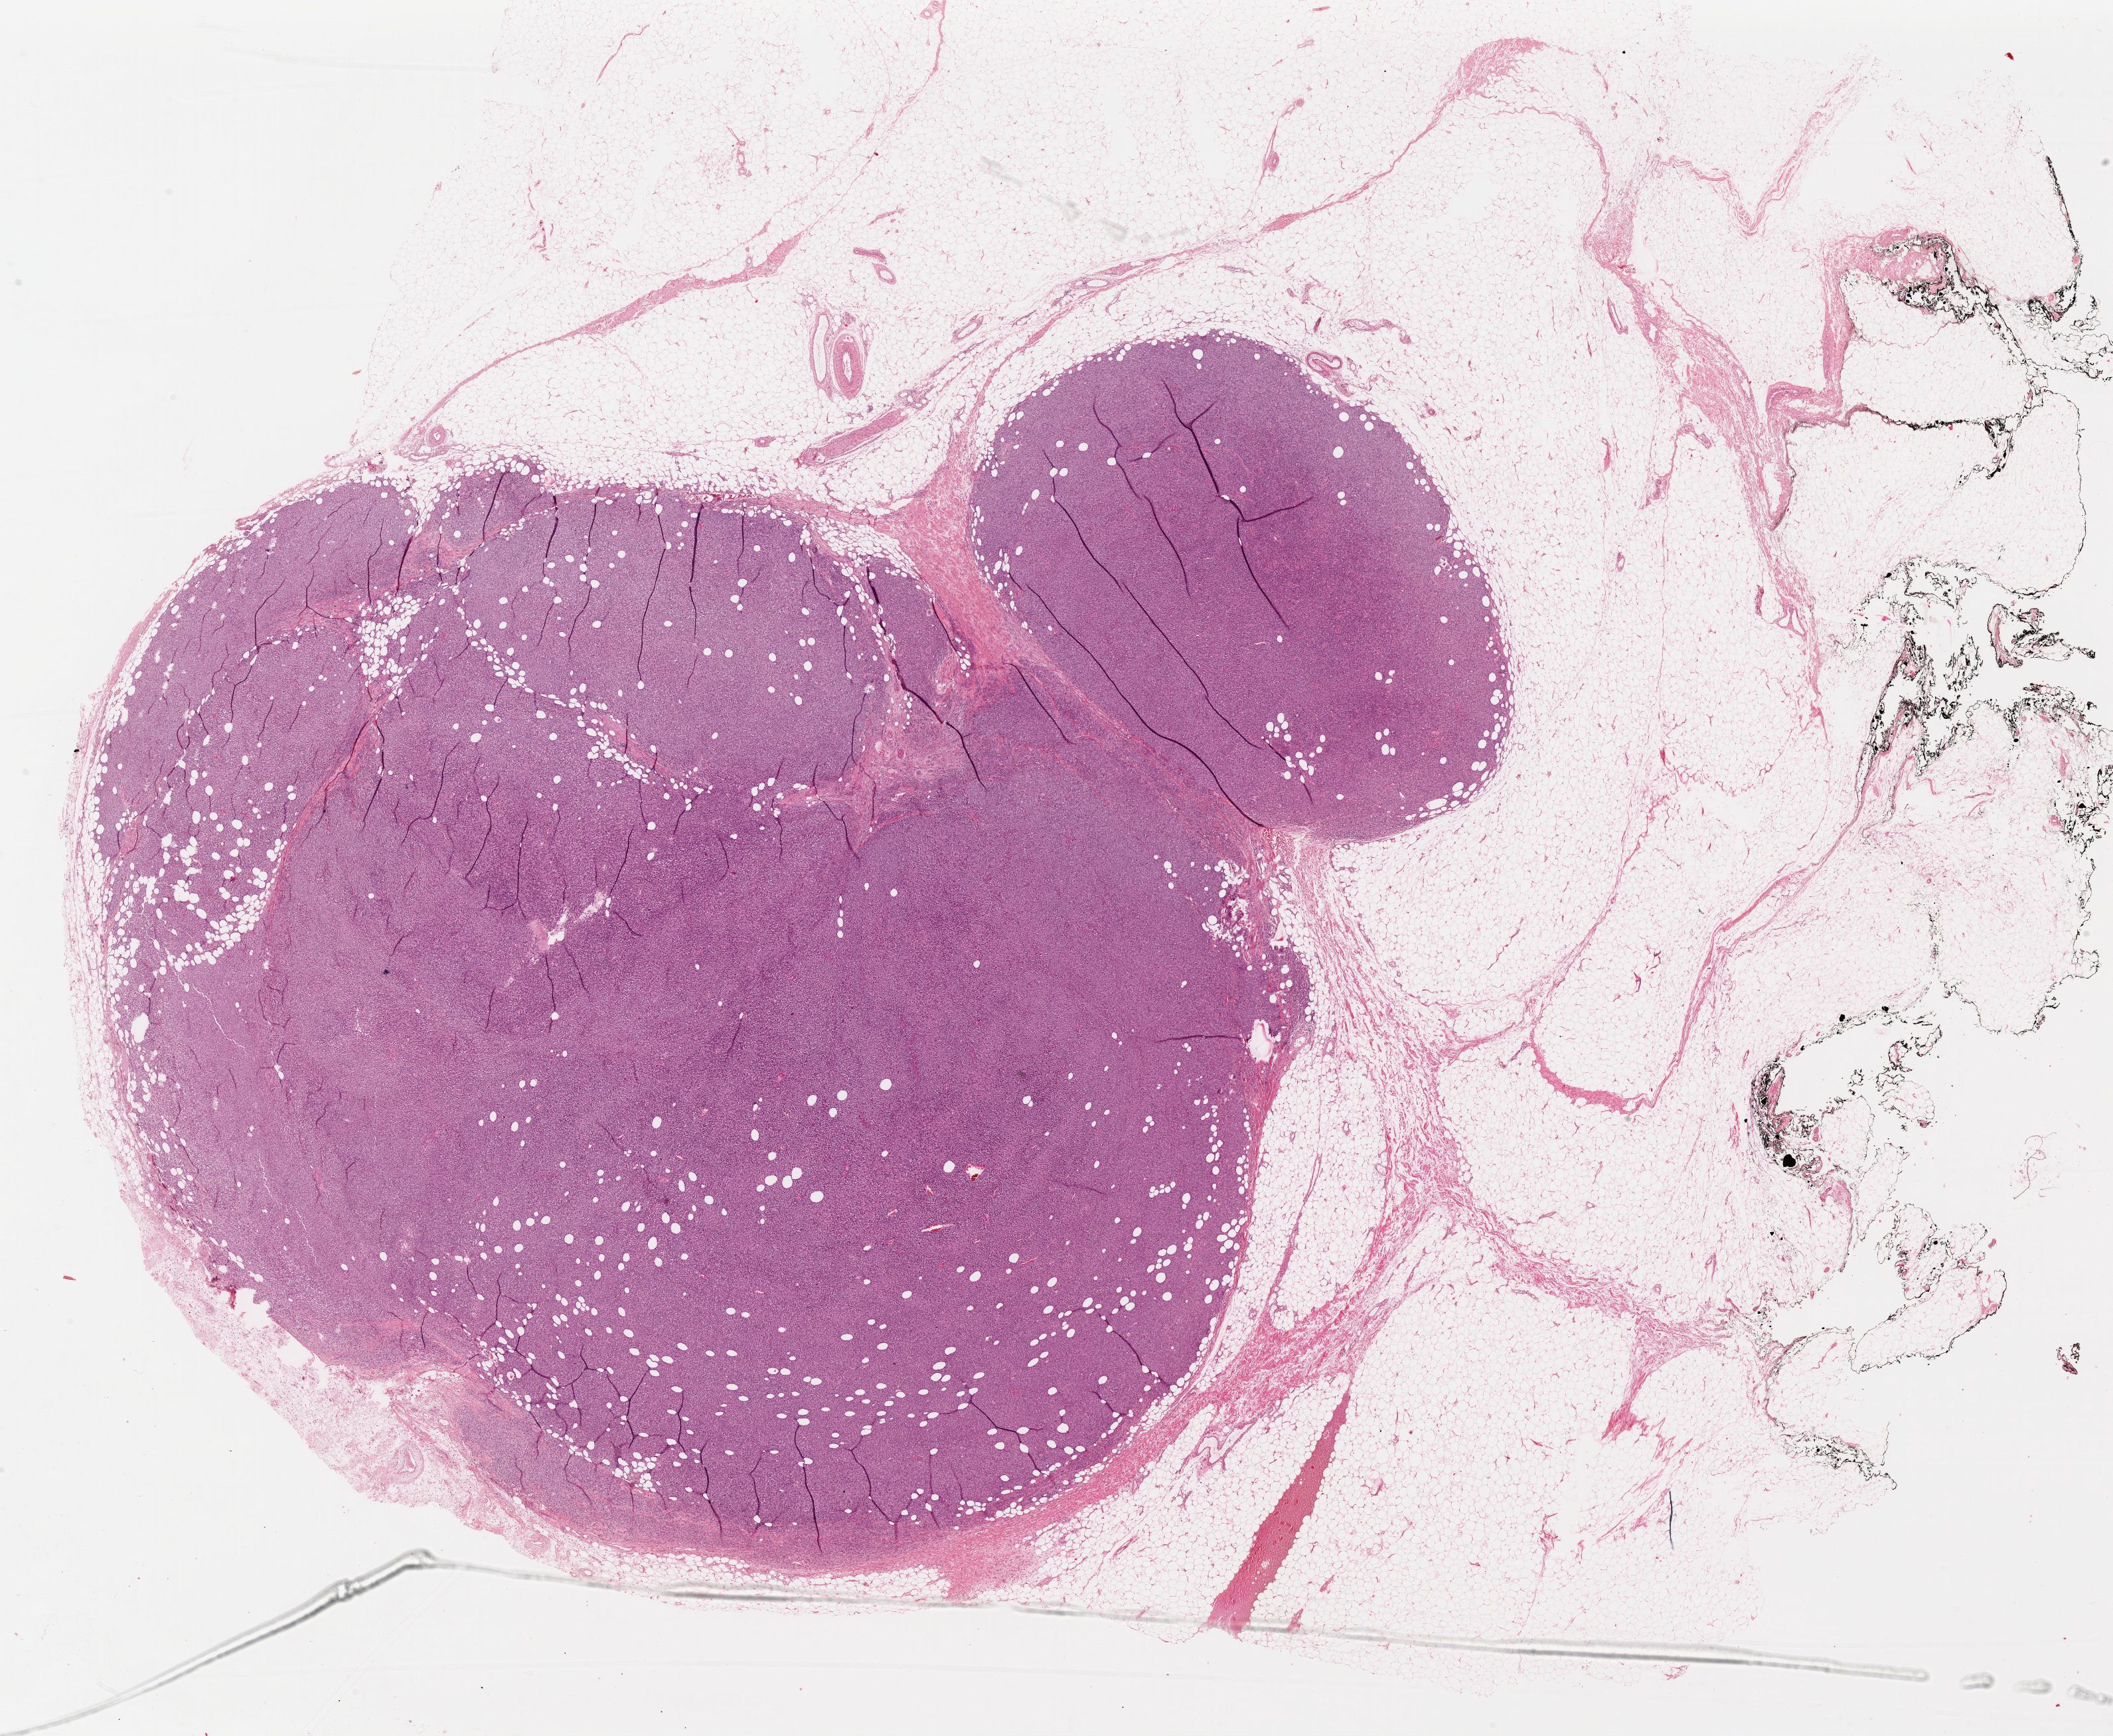
Whole-slide histology image, H&E-stained — shown as a low-resolution overview of the whole scanned area (about 25.0 x 20.6 mm); formalin-fixed paraffin-embedded (FFPE) diagnostic section; skin, primary tumour sample. Patient: female, age at initial diagnosis 66 years.
- diagnosis: Malignant melanoma, NOS